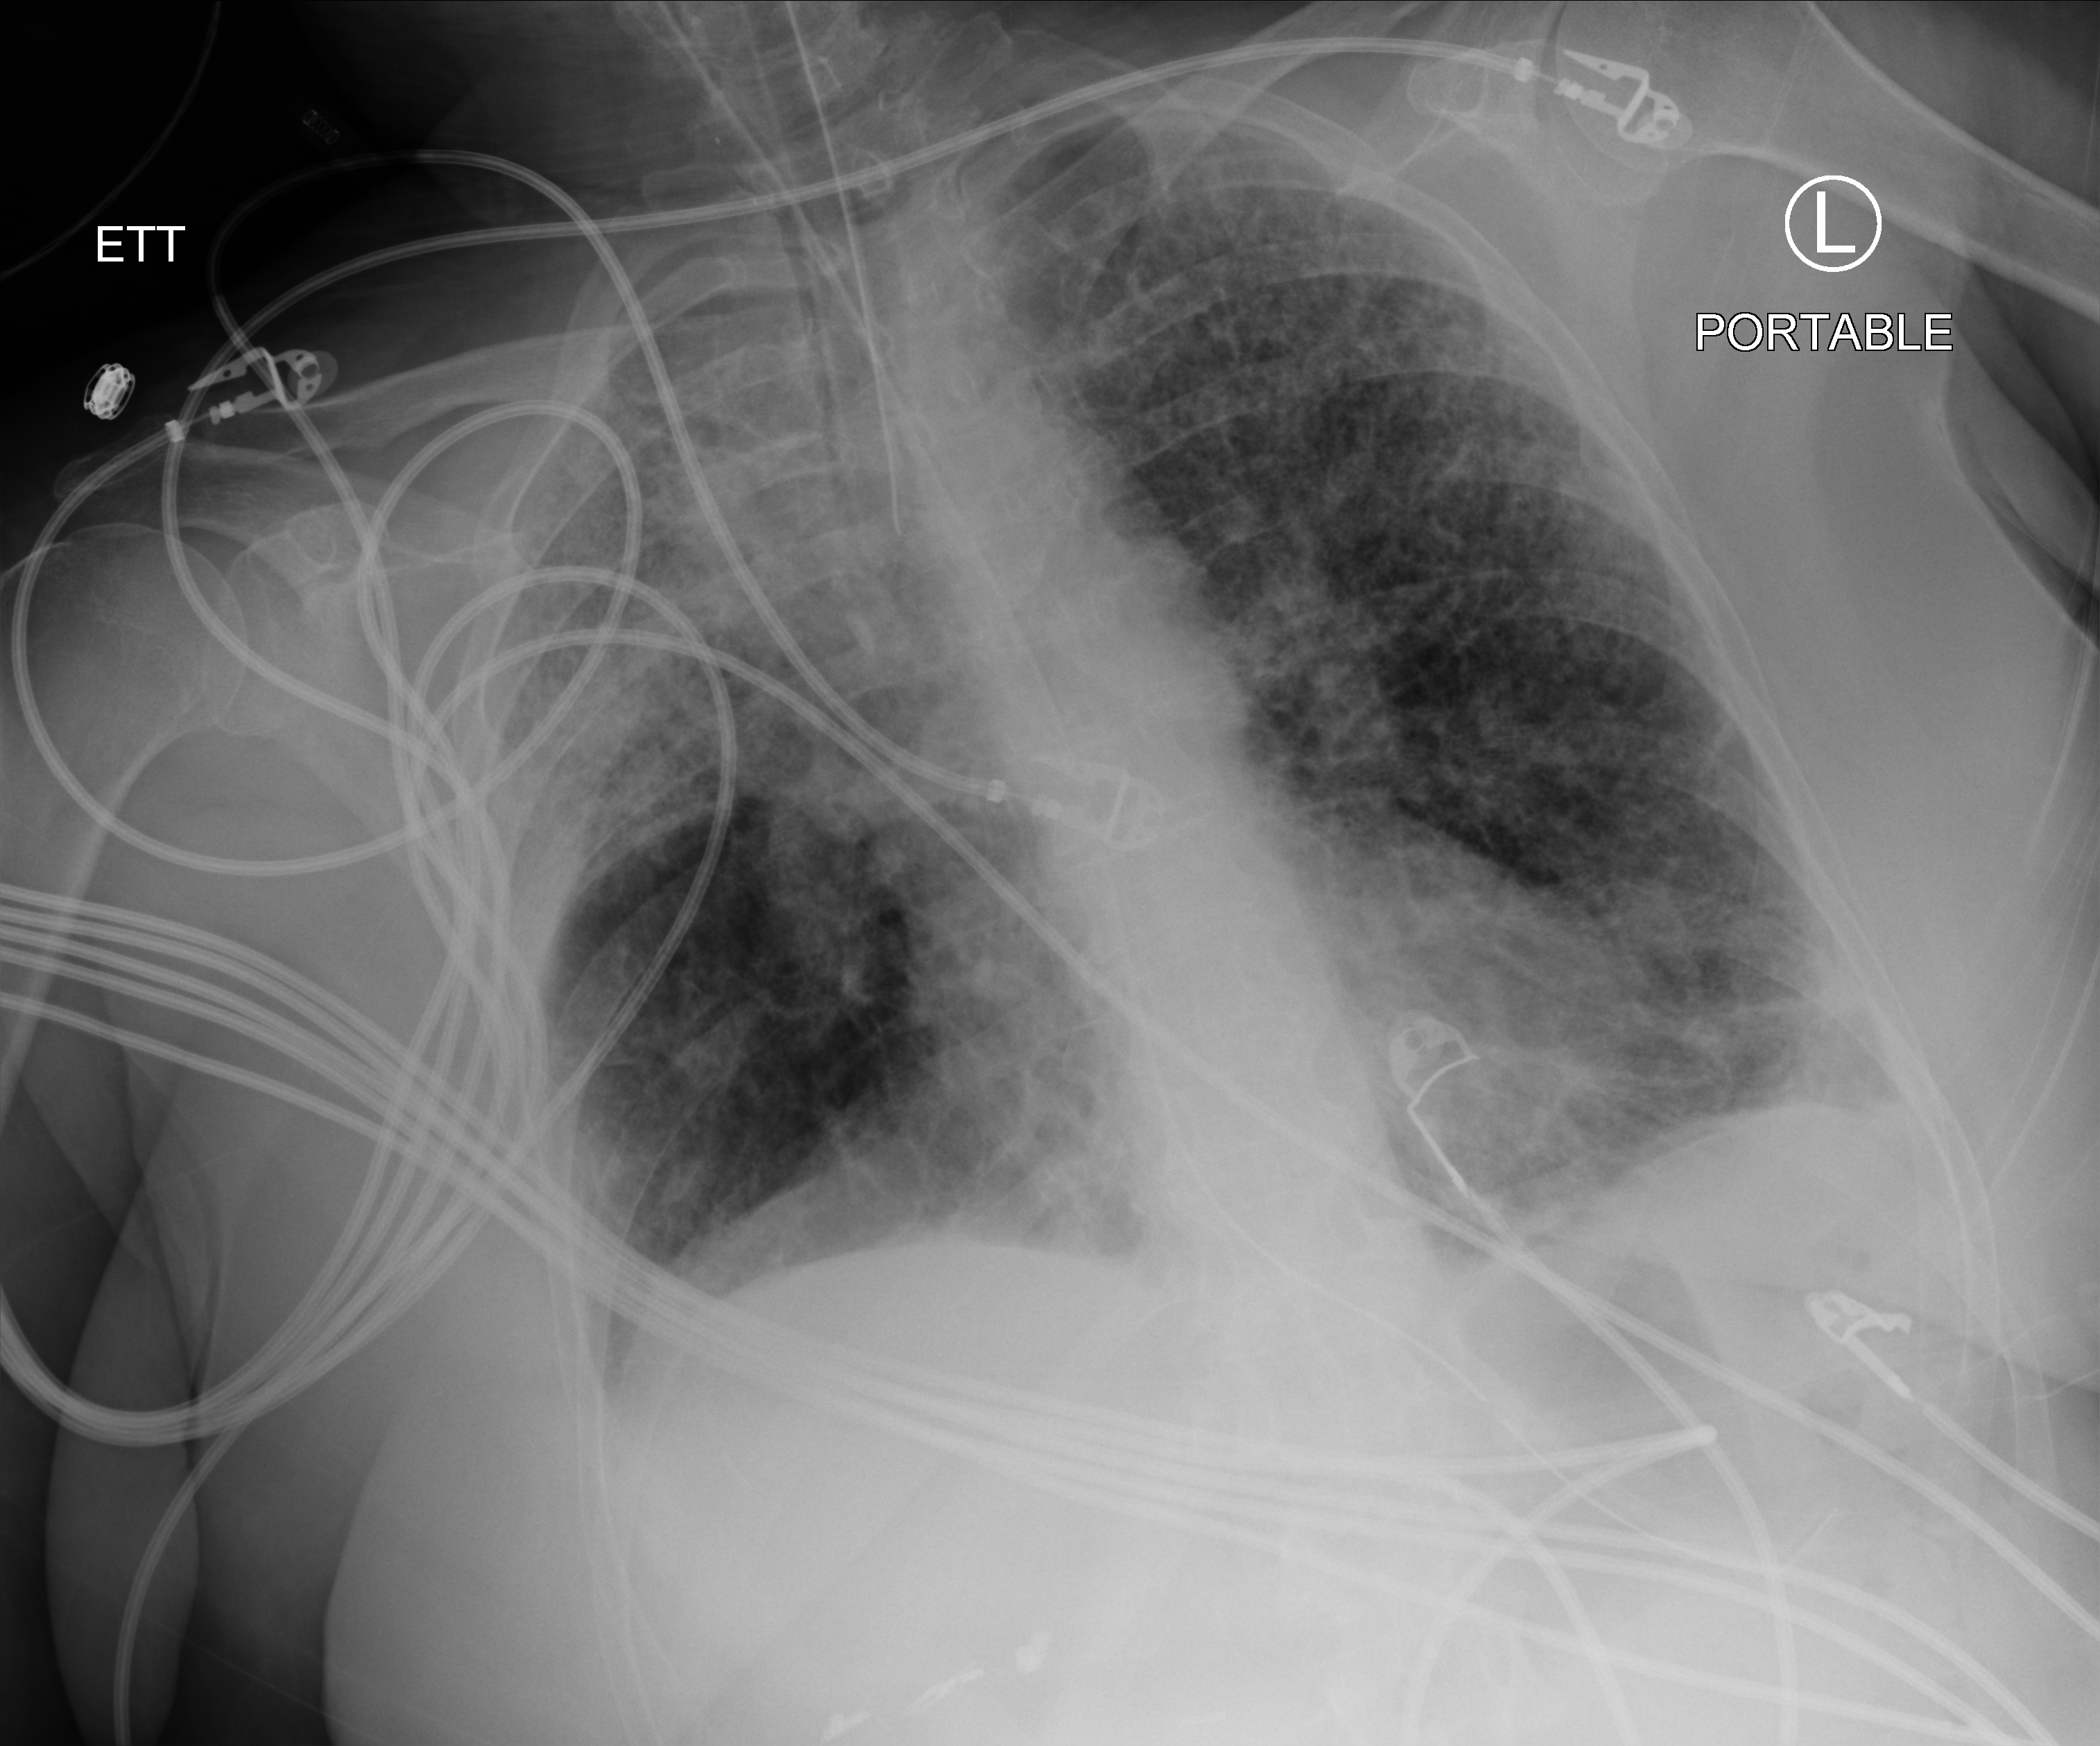
Portable chest radiograph, anteroposterior (AP) projection. Female patient hospitalised with COVID-19, age 60–74 years.
From the hospital-stay record, not from the radiograph (when in the stay this image was taken is not recorded): chronic kidney disease (admission record): no; admitted to intensive care during this hospital stay: yes; mechanically ventilated during this hospital stay: yes.